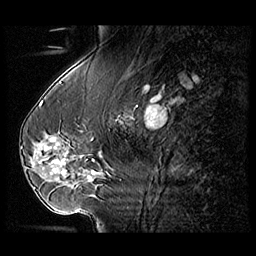
Breast MRI (dynamic contrast-enhanced), one sagittal slice; slice 43 of 104 in the series (ordered by position); 3 images stored at this slice position (order not interpretable as contrast timing); 1.5 T; TE 1.3 ms, TR 5.5 ms; 256 × 256 image matrix. Female patient, age 54 years. From the clinical record (not read from this slice): setting: breast cancer imaged before/during neoadjuvant chemotherapy; receptor status: HR-positive, HER2-negative.
Structures marked on this image (semi-automatic segmentation, software-assisted and operator-edited):
- analysis volume of interest (the breast-tissue region the enhancement analysis was run in; not a lesion): box from (x=28, y=127) to (x=104, y=182) px
- tumour enhancement mask (voxels above the 140 % enhancement threshold inside the analysis volume of interest): (x=46, y=138)–(x=64, y=173)